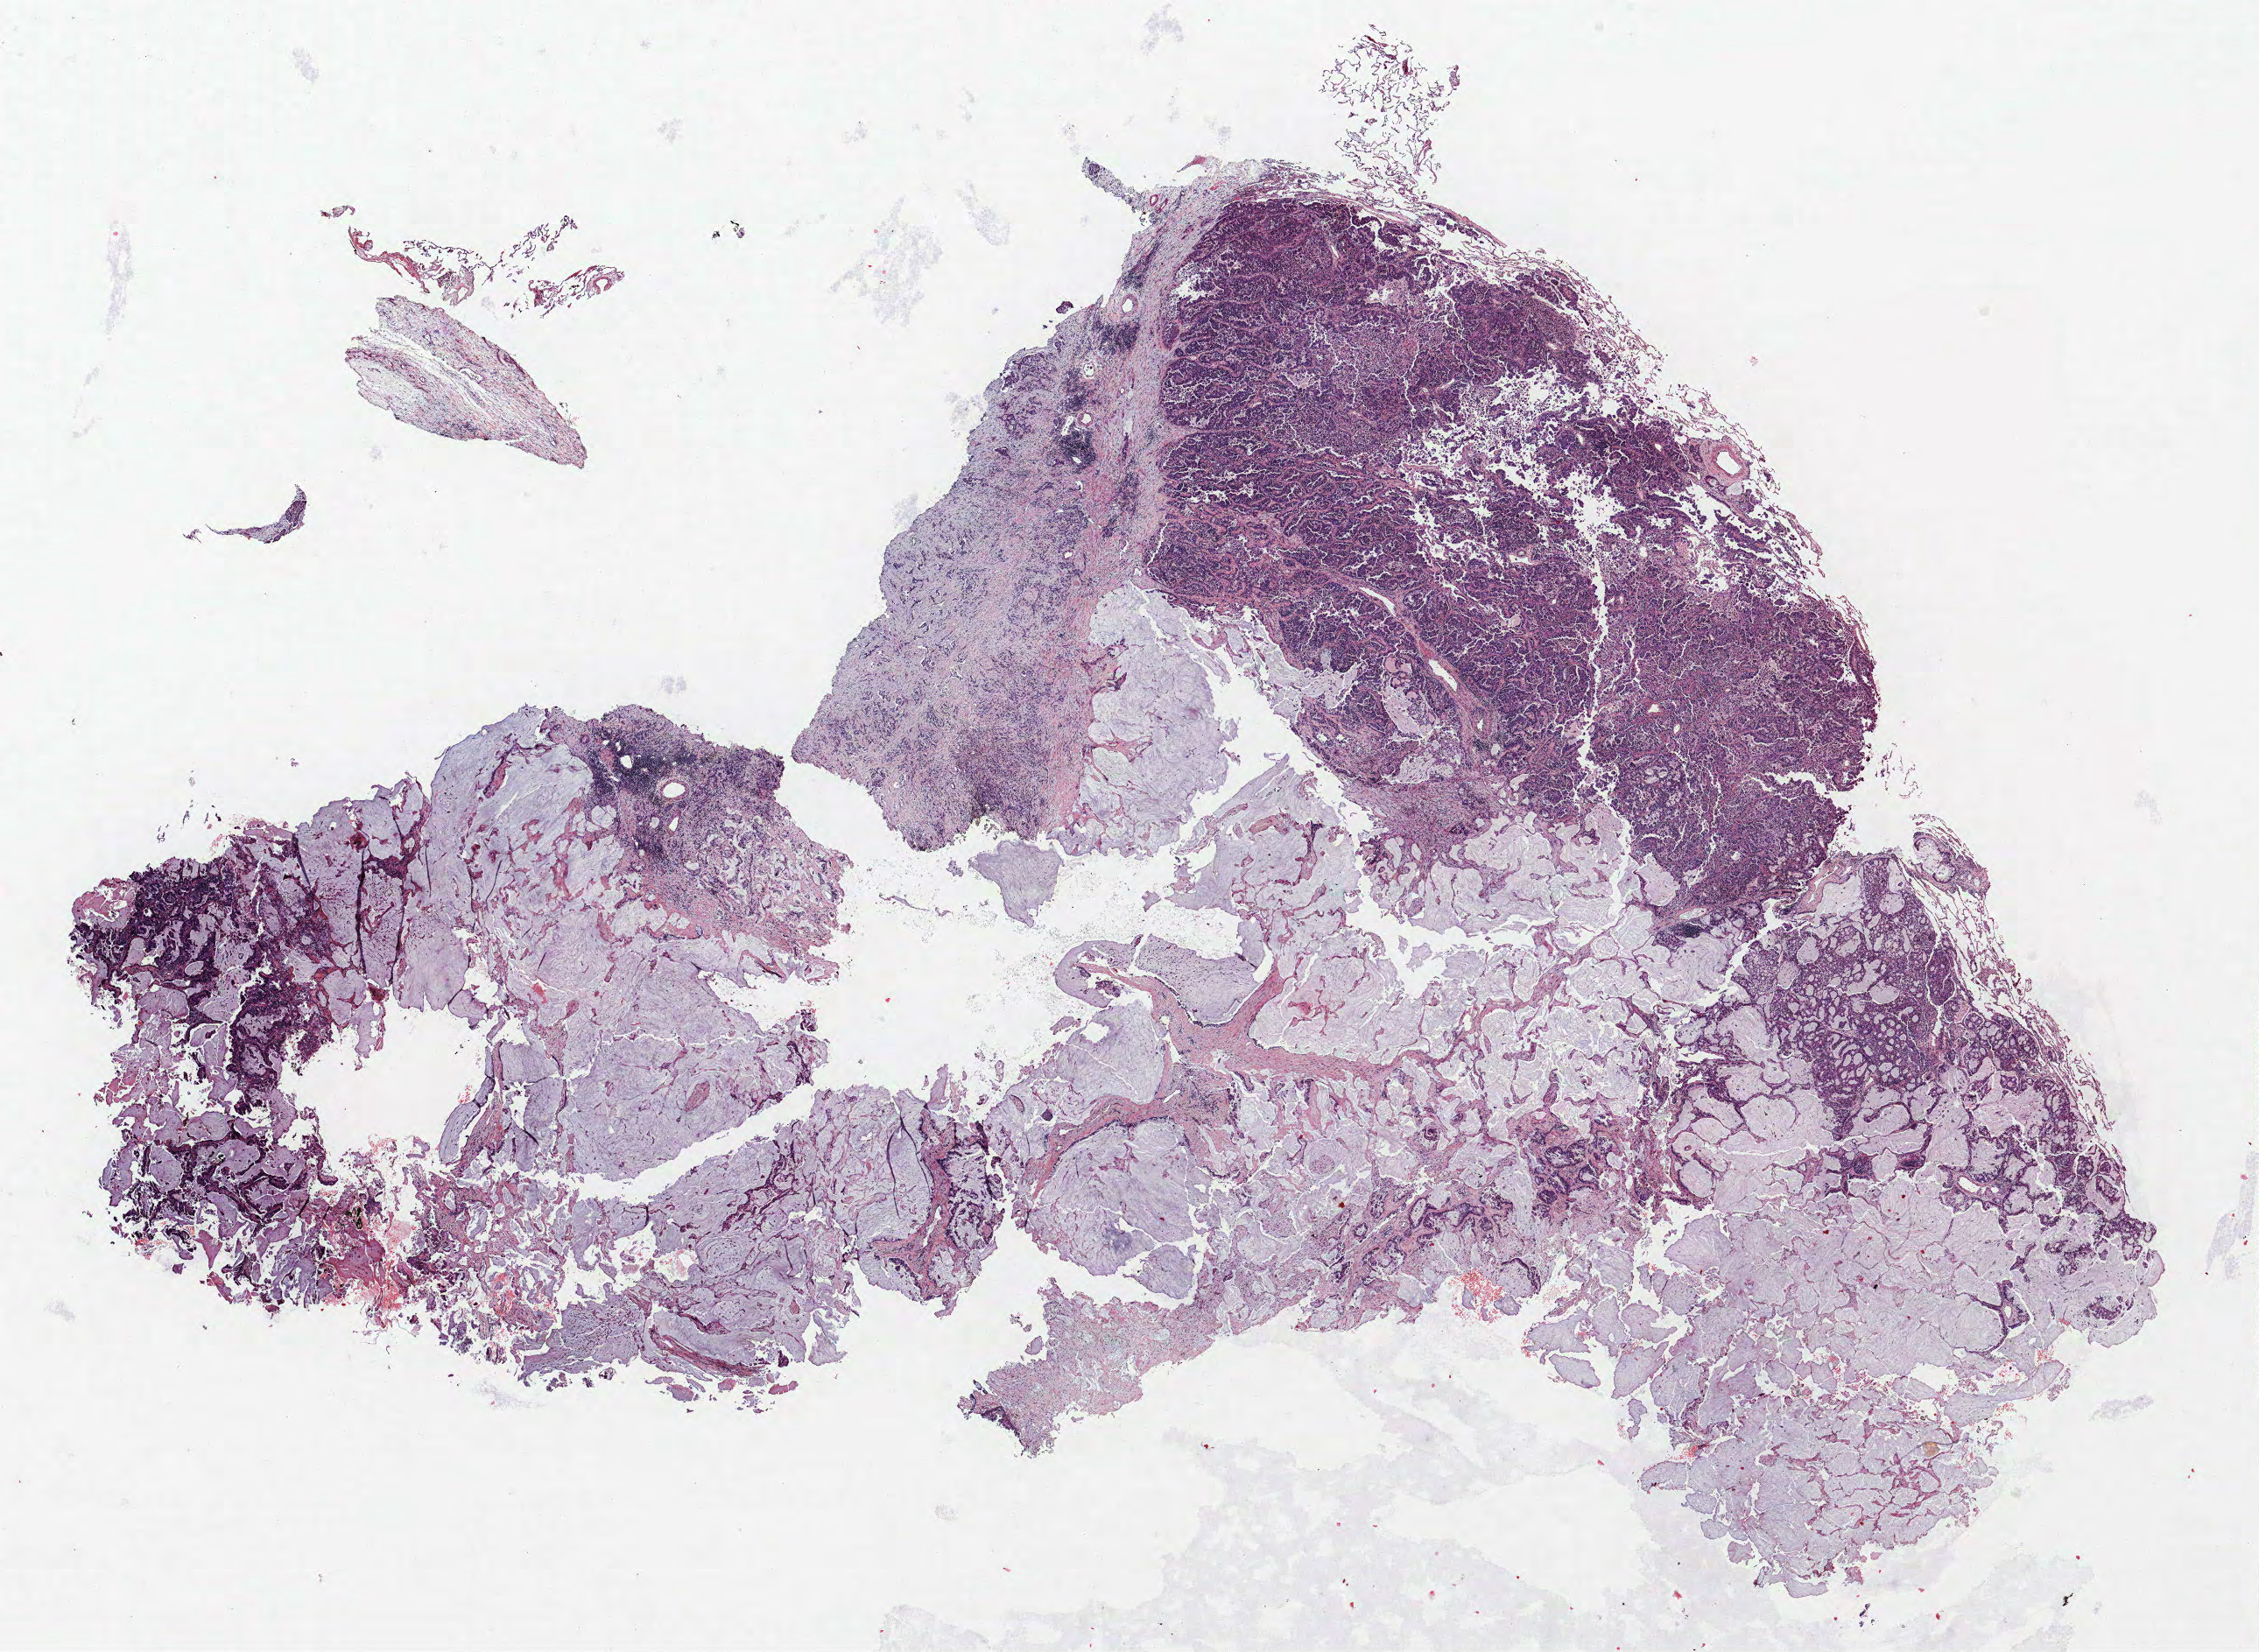
Hematoxylin and eosin (H&E) stained whole-slide image — whole scanned area (about 20.6 x 15.1 mm, acquisition: 40x scan) shown as a low-resolution overview. Formalin-fixed paraffin-embedded (FFPE) section. Lung tissue. Female patient, aged 63 at enrolment. Current smoker at enrolment. Grade: moderately differentiated (G2).
Tumour size (pathology): 28 mm. Participant's lung-cancer diagnosis: Mucinous adenocarcinoma (ICD-O-3 8480/3). Primary tumour location (clinical record): right lower lobe. Stage (AJCC 6th edition): IIA.